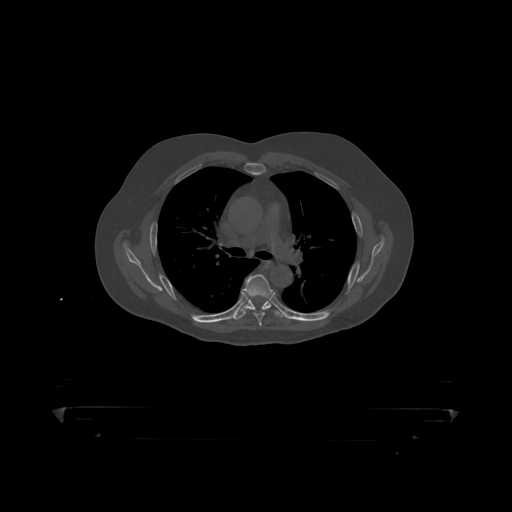
CT including the spine, one axial slice. Slice 311 of 390 in the series (ordered by position). Bone window (W 1800 / L 400 HU). 1.25 mm slice thickness. 512 × 512 image matrix. Male patient, age 60 years. From the clinical record (not read from this slice): primary cancer: prostate.
Annotated regions visible in this slice (semi-automatically segmented with operator editing):
- T5 vertebra: box from (x=242, y=275) to (x=276, y=319) px
- T6 vertebra: (x=235, y=298)–(x=281, y=317)